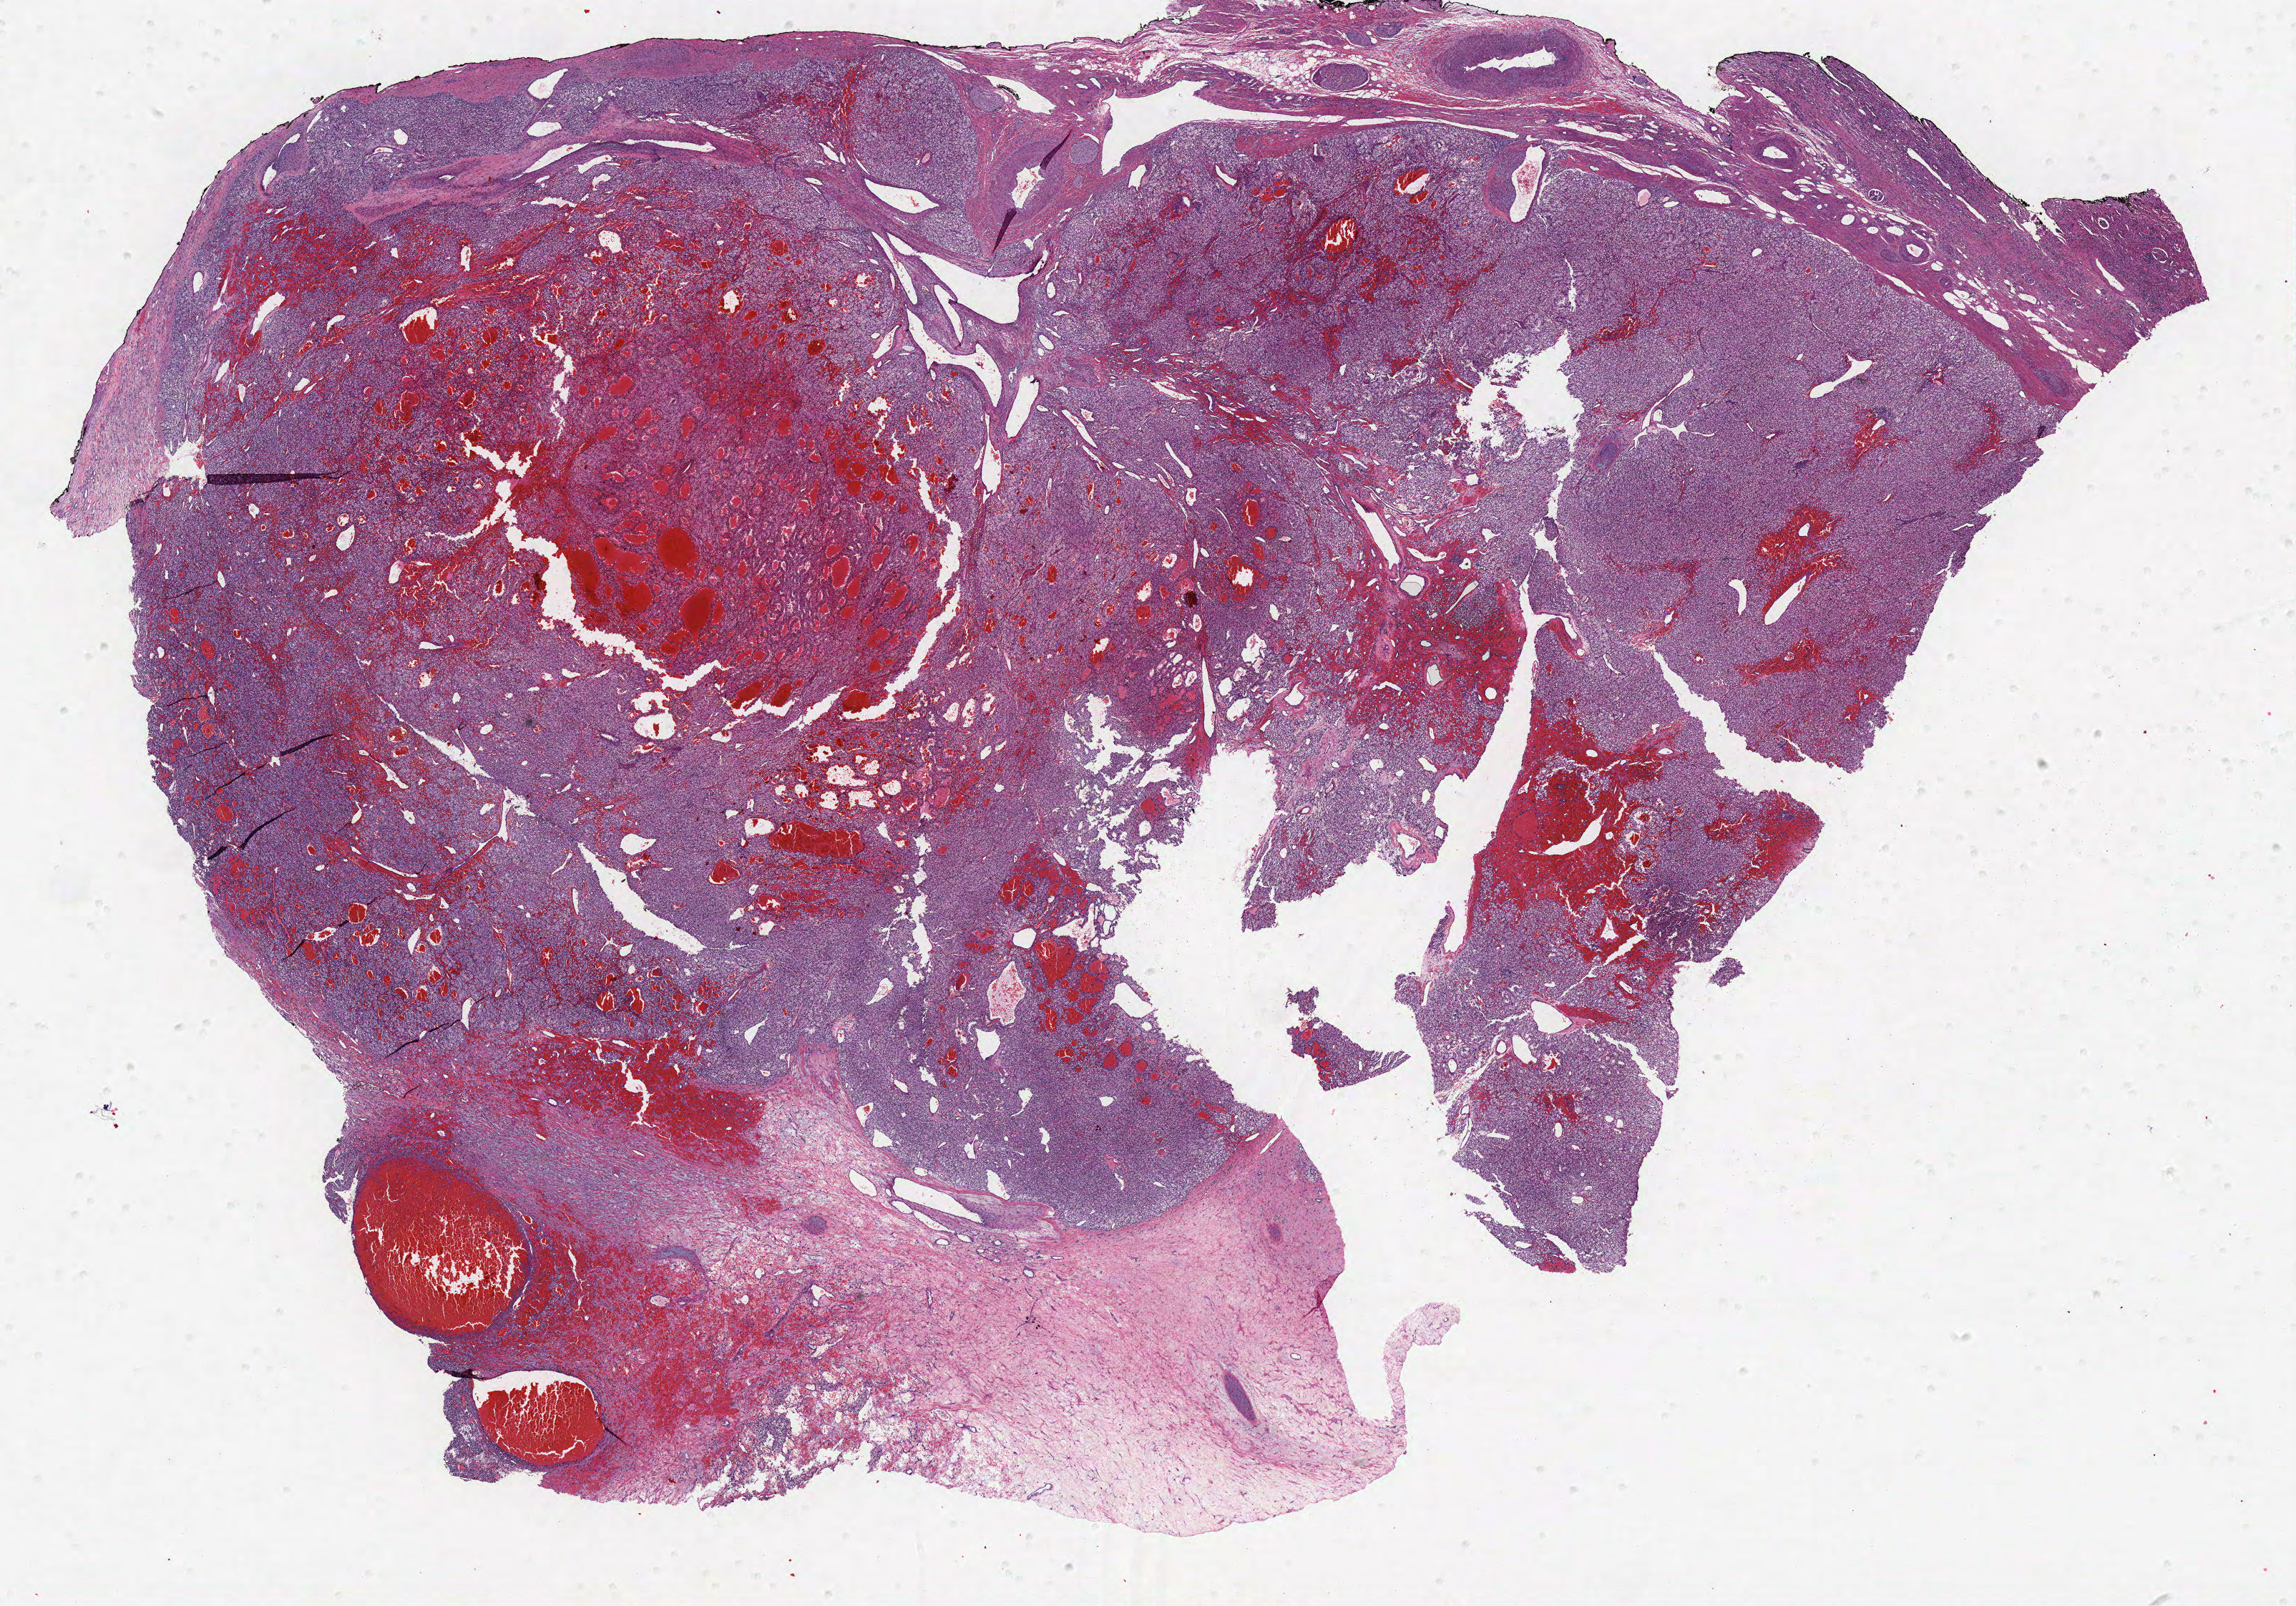
Digitized Hematoxylin and eosin (H&E) stained tissue section (whole slide) — a low-resolution overview of the entire scanned area, about 25.7 x 17.9 mm (acquisition: 40x scan); formalin-fixed paraffin-embedded (FFPE) diagnostic section; kidney, primary tumour sample. Patient: male, age at initial diagnosis 77 years. Histologic grade: G3 (poorly differentiated).
Pathologic diagnosis: Clear cell adenocarcinoma, NOS. AJCC pathologic stage: I.